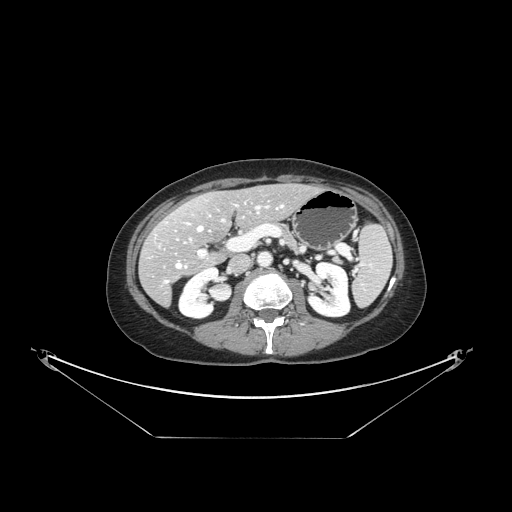
Contrast-enhanced abdominal CT, one axial slice; slice 73 of 148 in the series (ordered by position); reconstruction kernel STANDARD; 120 kVp; intravenous contrast given; soft-tissue window (W 400 / L 40 HU); 2.5 mm slice thickness; 512 × 512 image matrix, field of view 500 × 500 mm. Female patient, age 73 years. Case-level facts recorded for this patient, not image findings: diagnosis: colorectal cancer liver metastases, imaged before liver resection; multiple liver metastases: no; largest metastasis: 1 cm; chemotherapy before resection: yes.
Annotated regions visible in this slice (outlined manually by an expert reader):
- hepatic veins: box from (x=158, y=205) to (x=284, y=283) px
- liver: (x=140, y=186)–(x=317, y=304)
- planned liver remnant (the part of the liver to remain after resection): (x=168, y=185)–(x=316, y=245)
- portal vein (with intrahepatic branches): (x=189, y=205)–(x=261, y=258)